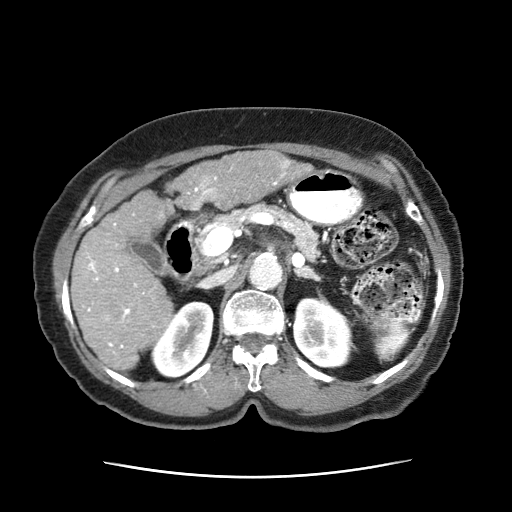
Contrast-enhanced abdominal CT (liver protocol), one axial slice; position 25 of 63 along the scan axis; intravenous contrast given; soft-tissue window (W 400 / L 40 HU); 512 × 512 image matrix. Female patient, age 79 years. From the clinical record (not read from this slice): diagnosis: hepatocellular carcinoma (patient treated with transarterial chemoembolisation; whether this scan precedes or follows treatment is not stated here); TNM stage (as recorded): Stage-II; Child-Pugh class: B.
Structures marked on this image (semi-automatically segmented with operator editing):
- abdominal aorta: bounding box <249,252,281,289> (left, top, right, bottom; pixels)
- liver parenchyma outside the tumour (the mass and vessels are separate outlines, so this box may not span the whole liver): <71,189,176,372>
- mass: <176,151,309,208>
- liver vessels: <82,172,286,354>